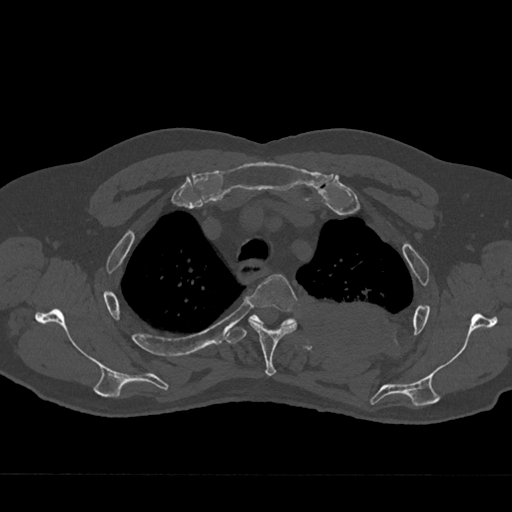
CT including the spine, one axial slice. Position 553 of 797 along the scan axis. 120 kVp. Bone window (W 1800 / L 400 HU). 0.5 mm slice thickness. 512 × 512 image matrix. Male patient, age 75 years. From the clinical record (not read from this slice): primary cancer: renal; vertebrae with lytic lesions (as recorded): T4.
Outlined on this slice (semi-automatic segmentation, software-assisted and operator-edited):
- T3 vertebra: box from (x=247, y=274) to (x=299, y=376) px
- T4 vertebra: (x=226, y=314)–(x=297, y=344)